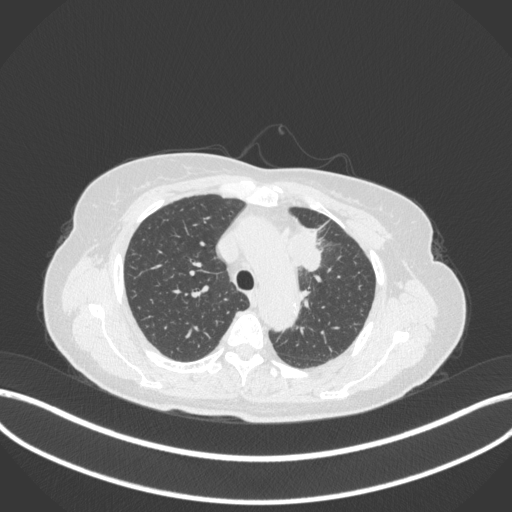
Chest CT, one axial slice; position 246 of 368 along the scan axis; 120 kVp; lung window (W 1500 / L -600 HU); 1 mm slice thickness; 512 × 512 image matrix. Patient: female, 65 years. From the clinical record (not read from this slice): clinical TNM (as recorded): T2a N0 M0.
Annotated regions visible in this slice (bounding box drawn by a radiologist):
- lung tumour (recorded histology: adenocarcinoma): box from (x=285, y=225) to (x=325, y=275) px